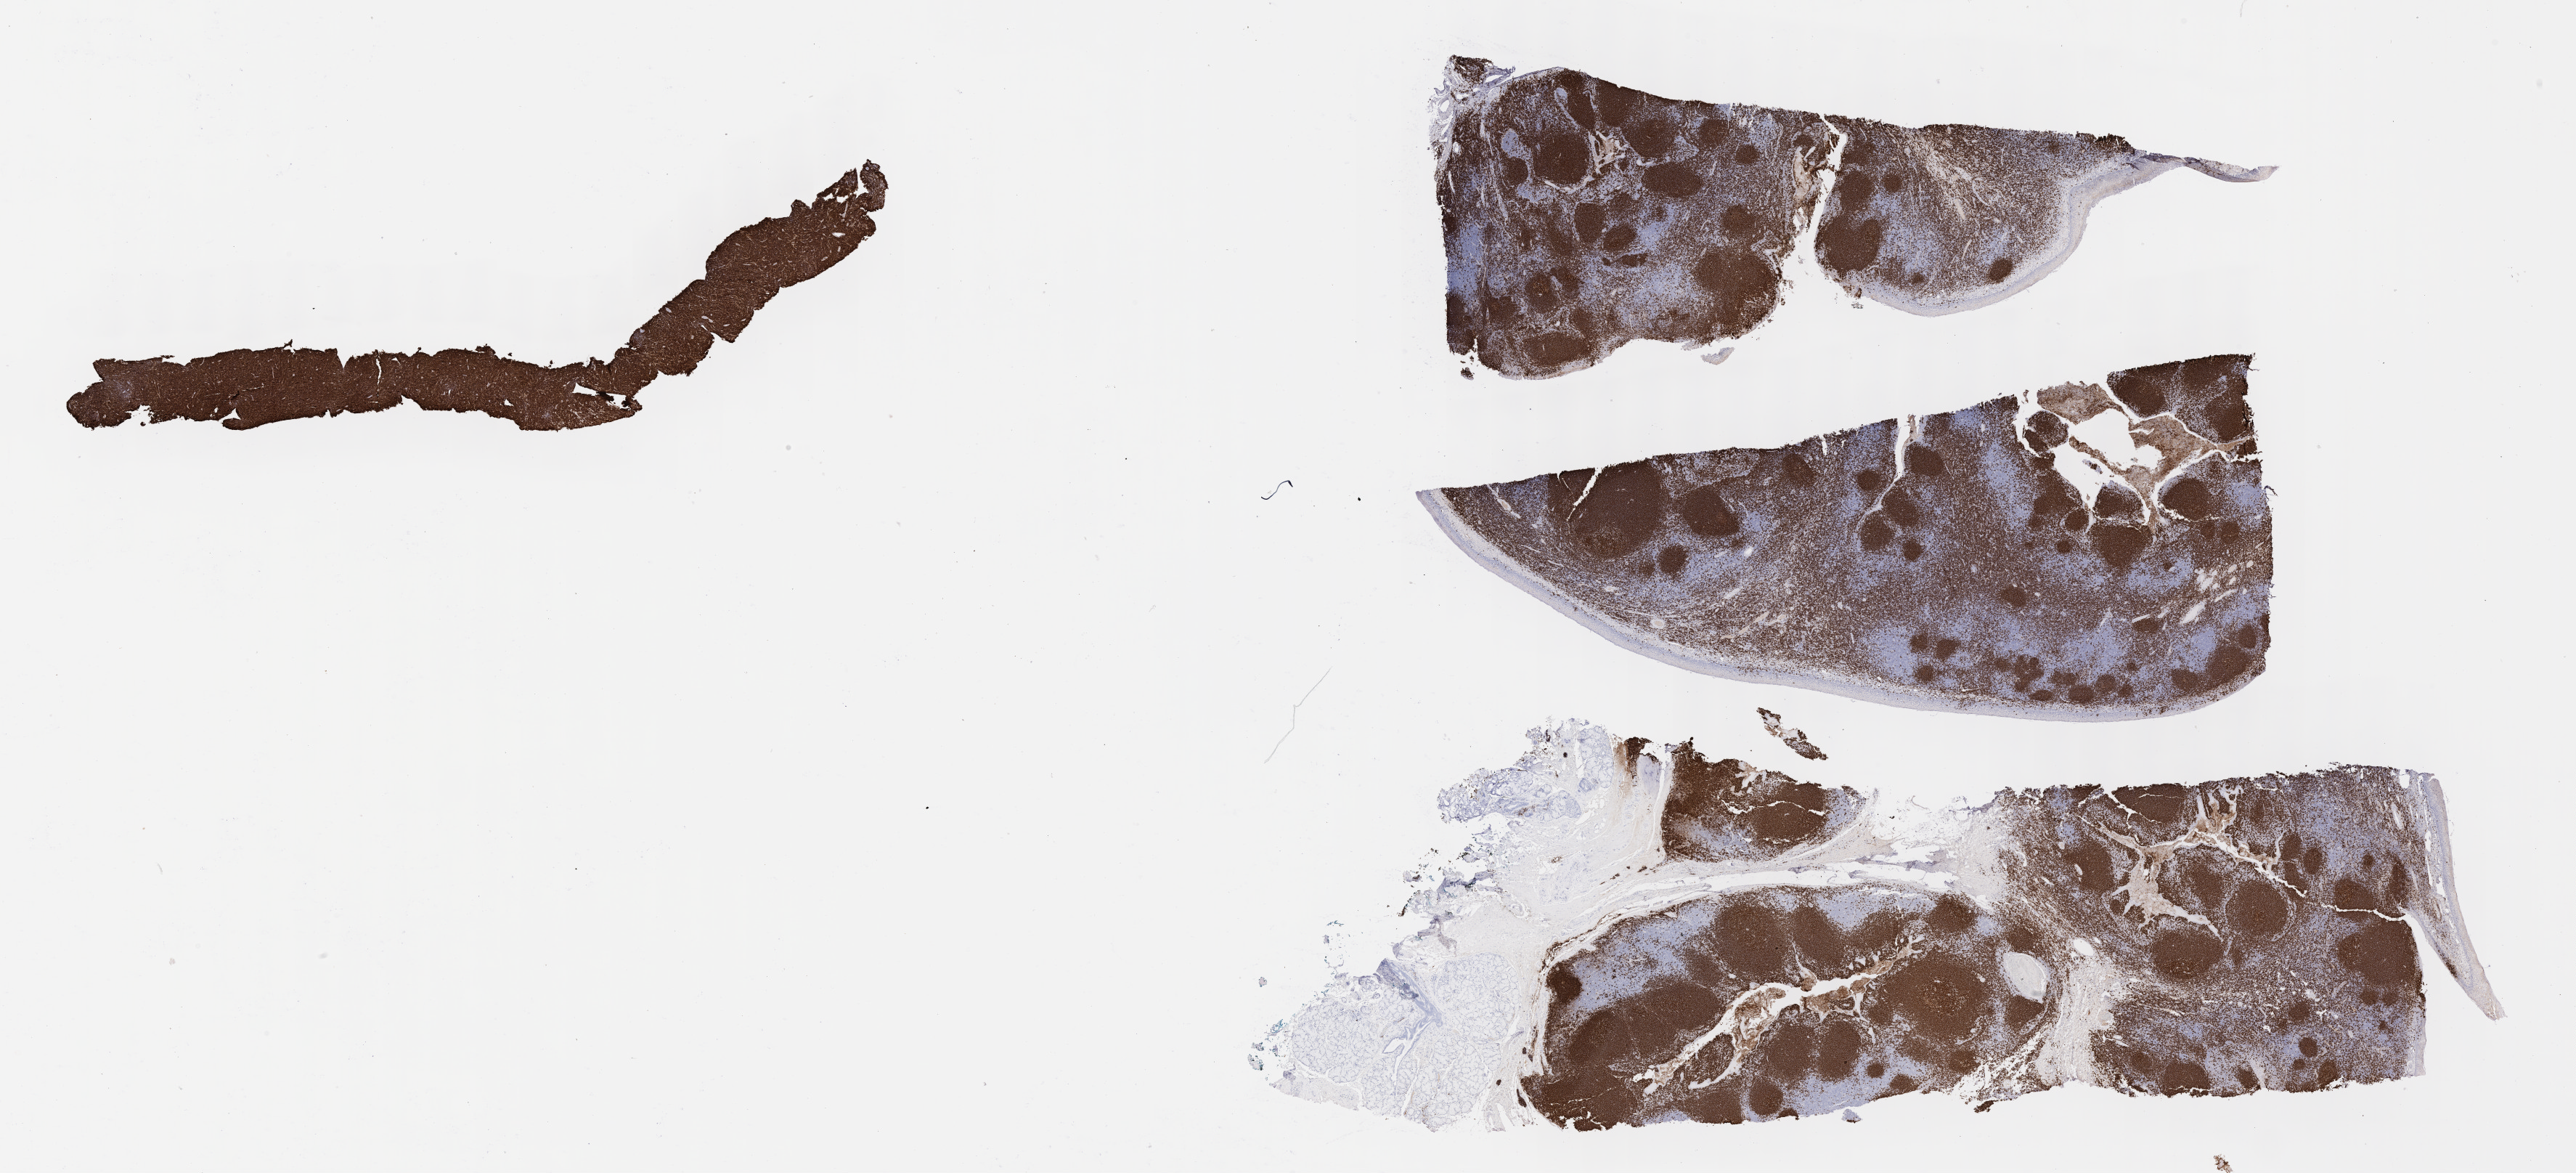
Immunohistochemistry (IHC) whole-slide image stained for CD20 — a low-resolution overview of the entire scanned area, about 28.7 x 13.1 mm; tumor tissue; anatomic site: kidney. Male patient; age at initial diagnosis 9 years.
• histologic diagnosis: Burkitt lymphoma, NOS